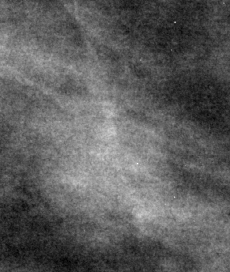
Region of interest cut from a scanned film mammogram (one marked finding), right breast, CC view, BI-RADS breast density category 2 (scale 1–4).
Finding: mass, shape round, margins circumscribed; BI-RADS assessment category 3; pathology (as recorded): benign.